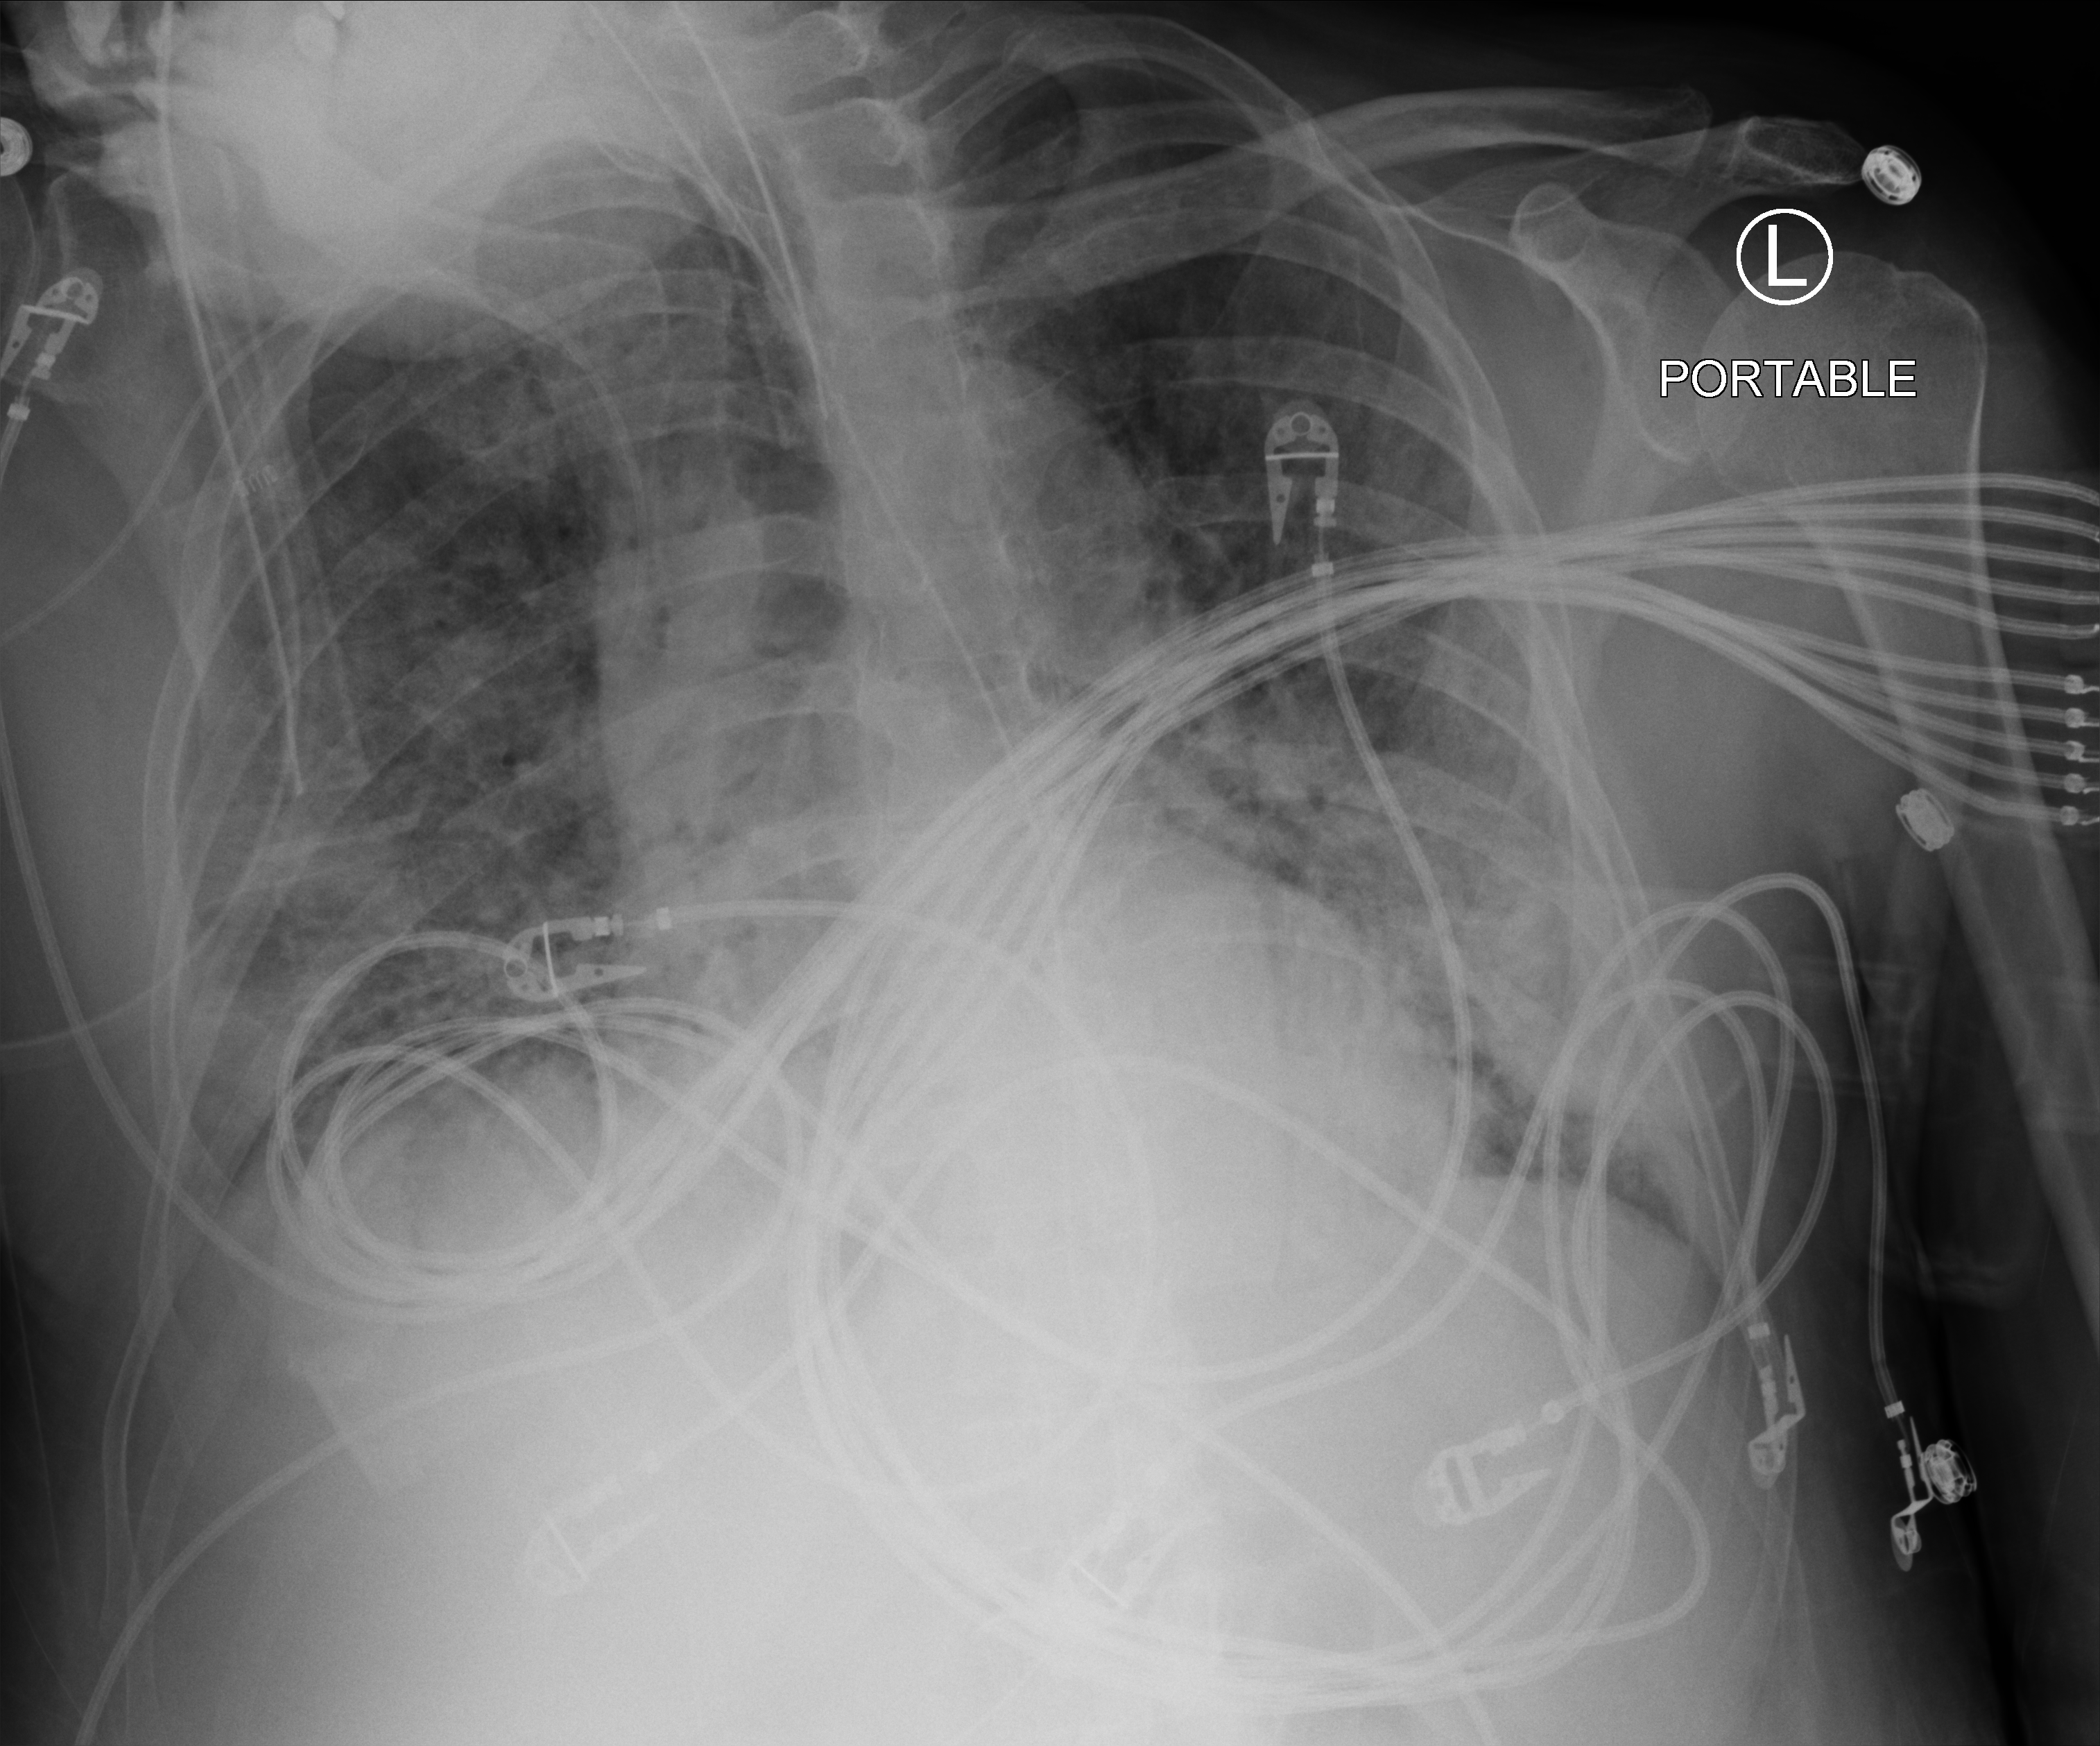
Bedside chest radiograph (computed radiography), anteroposterior (AP) projection. Patient hospitalised with COVID-19; male, aged 60–74 years.
Hospital-stay facts (about this admission, not read from this image; timing relative to this image not recorded):
- mechanically ventilated during this hospital stay: yes
- admitted to intensive care during this hospital stay: yes